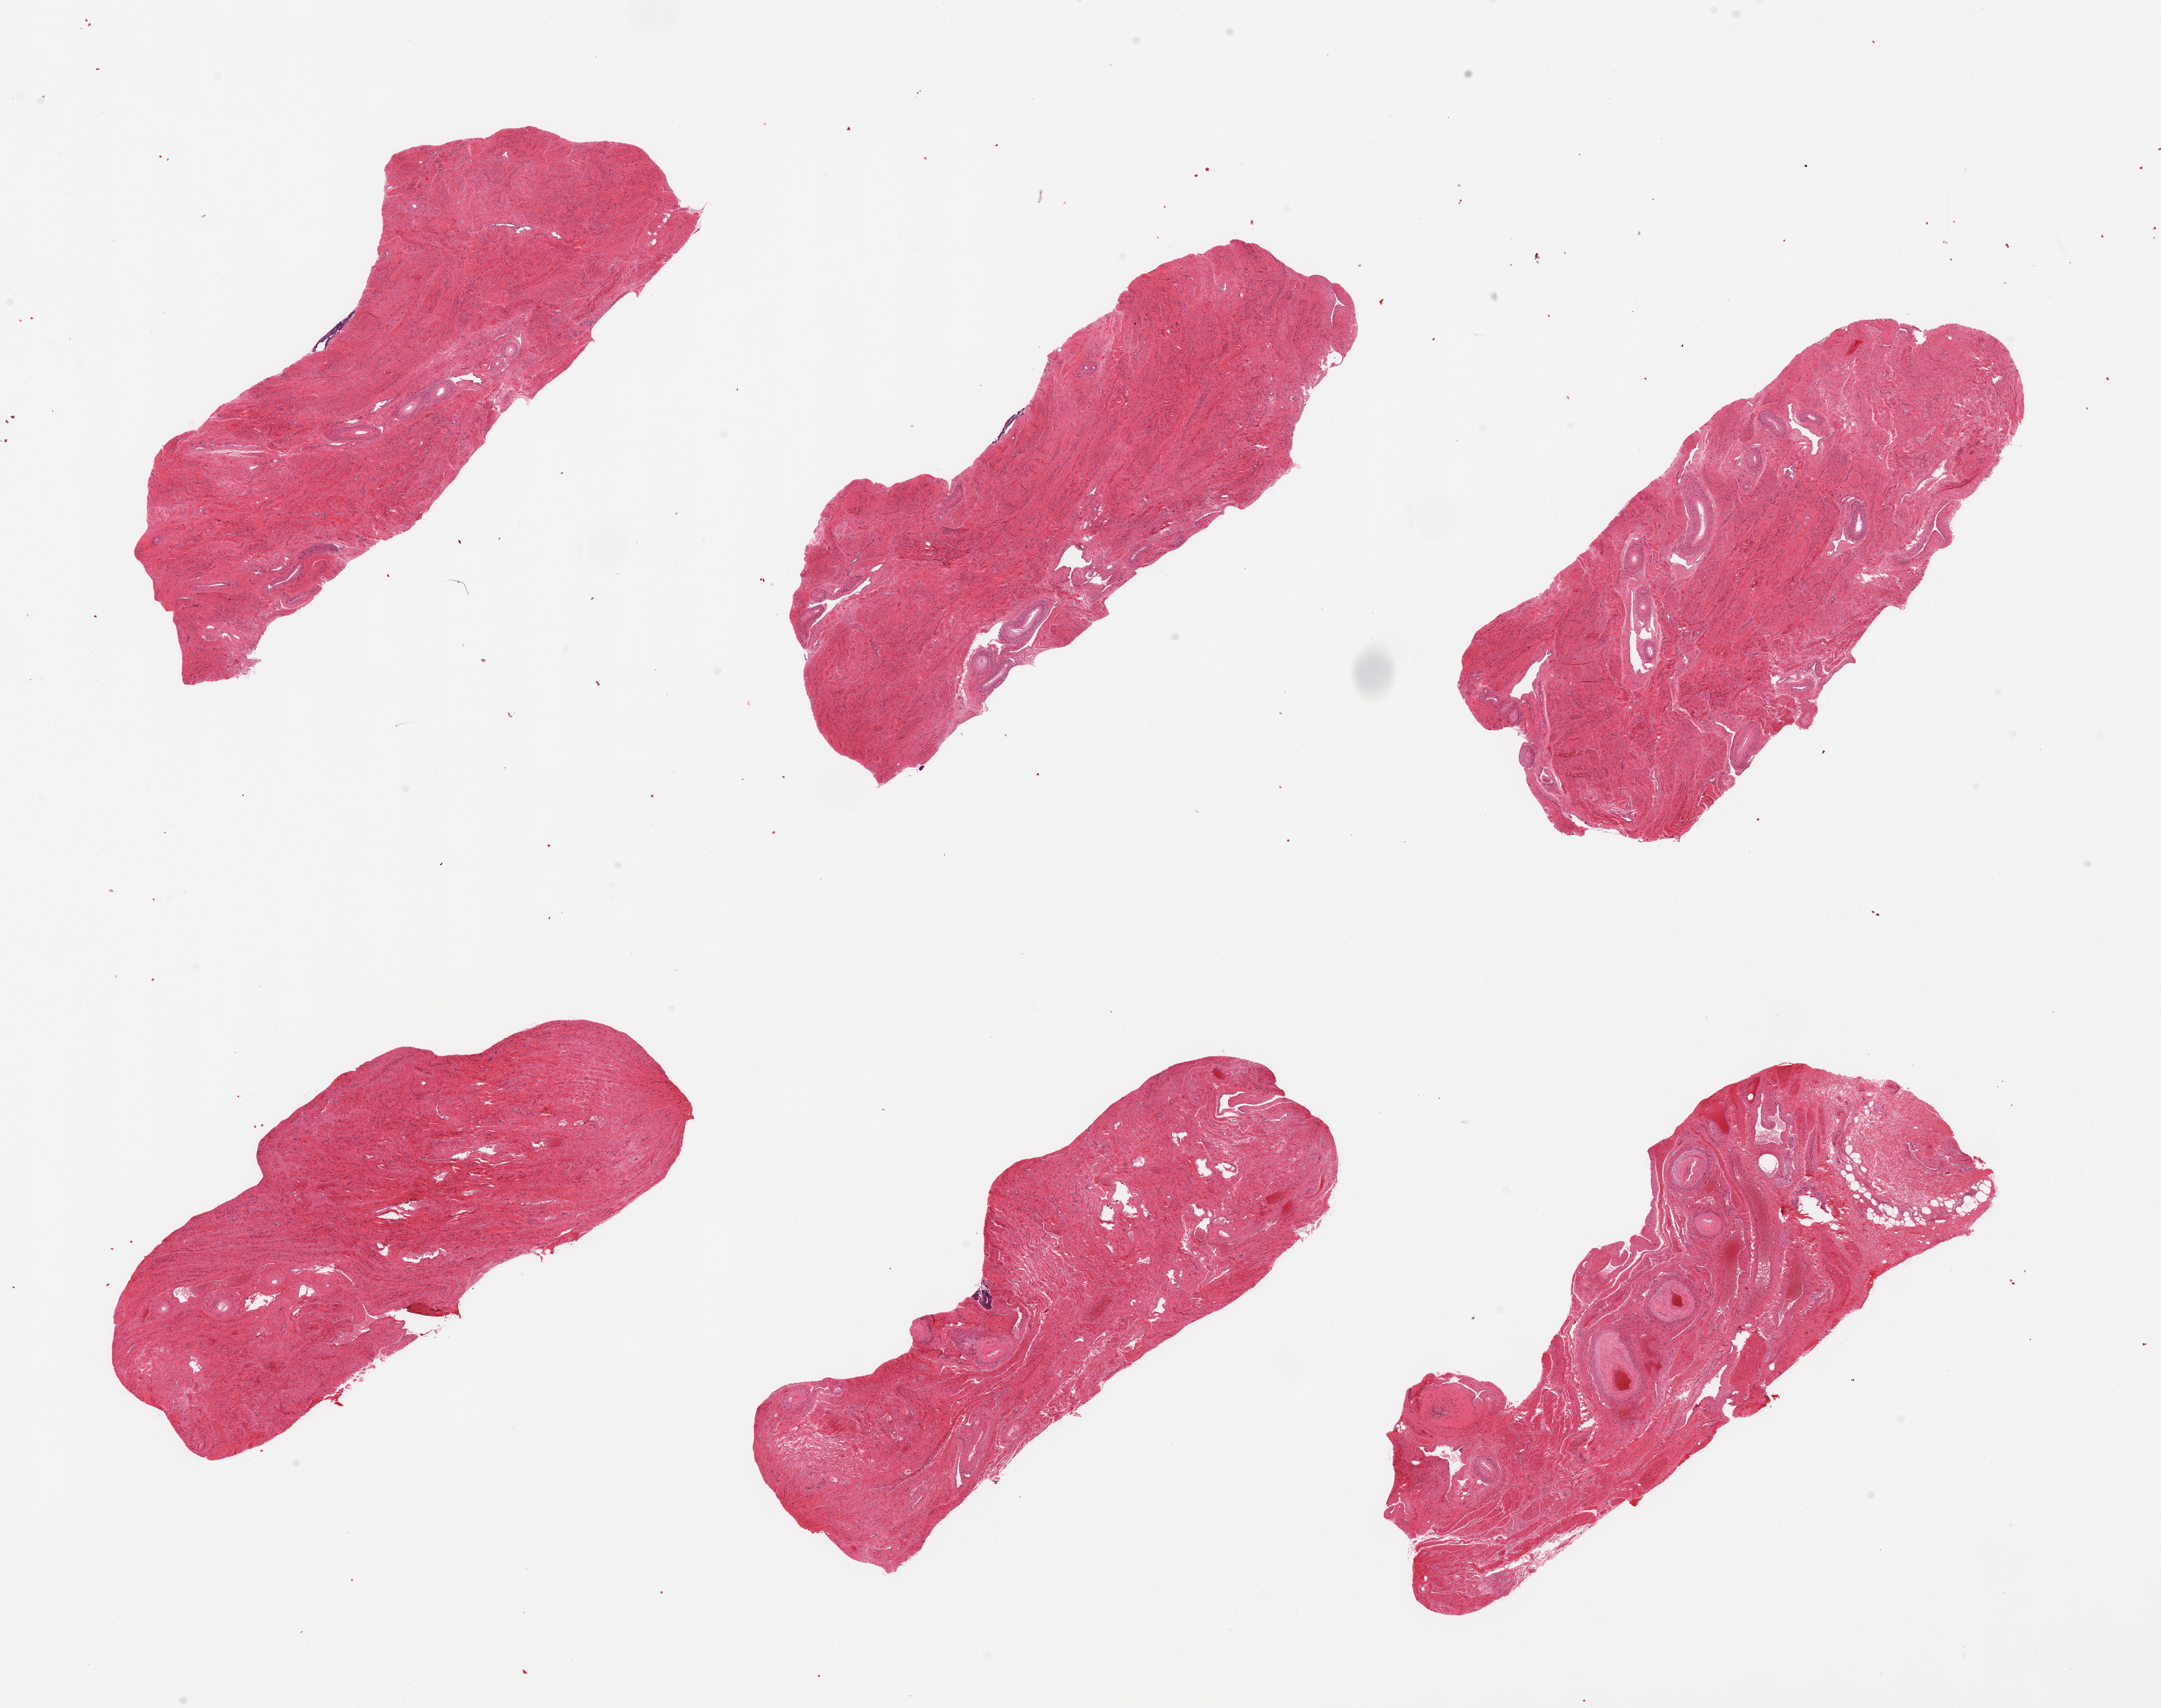
Whole-slide image, haematoxylin and eosin stain, a low-resolution overview of the entire scanned area, about 25.6 x 20.2 mm. PAXgene-fixed paraffin-embedded (PFPE) section. Target tissue: vagina. Tissue donor sample. Female donor.
Review note (as recorded): 6 pieces, all stroma, squamous mucosa completely sloughed/atrophic.